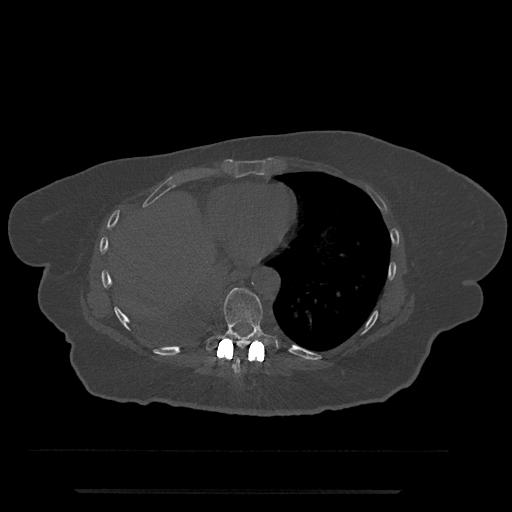
CT including the spine, one axial slice; position 344 of 797 along the scan axis; 120 kVp; bone window (W 1800 / L 400 HU); 0.5 mm slice thickness; 512 × 512 image matrix, field of view 440 × 440 mm. Female patient, age 51 years. From the clinical record (not read from this slice): primary cancer: neuro.
Annotated regions visible in this slice (semi-automatically segmented with operator editing):
- T8 vertebra: bounding box <233,349,264,374> (left, top, right, bottom; pixels)
- T9 vertebra: <205,287,277,354>